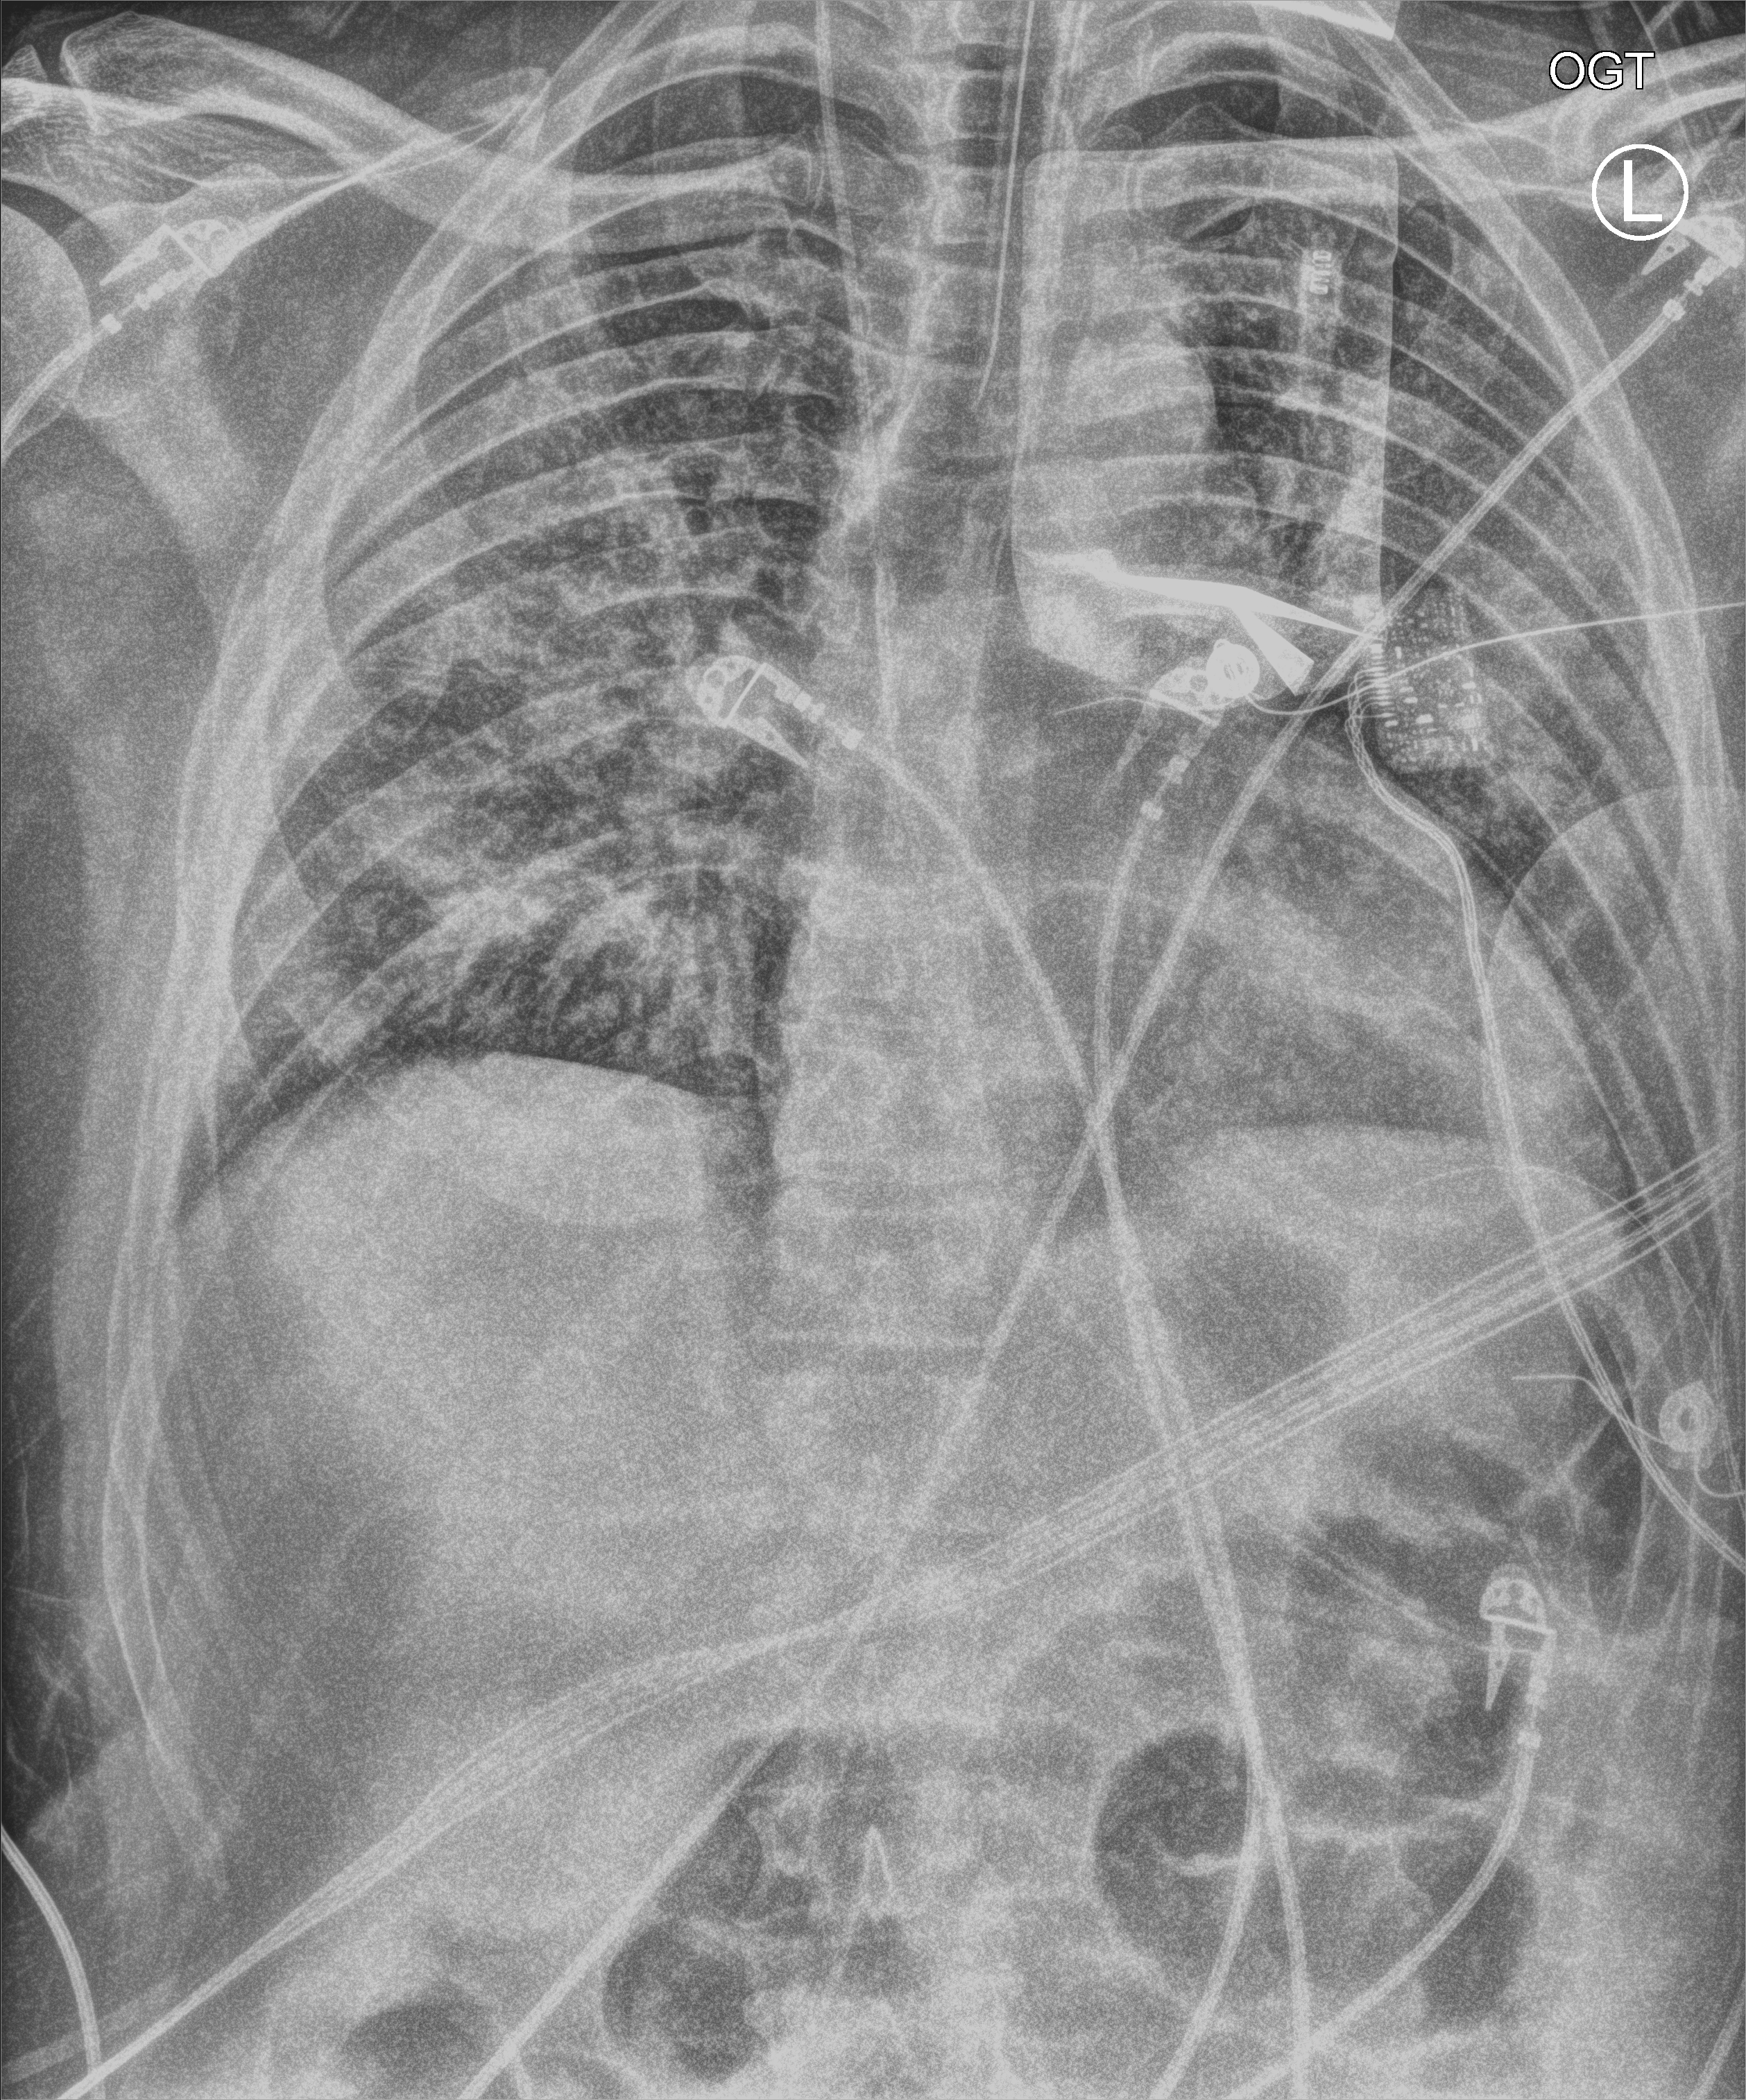
Portable chest radiograph; anteroposterior (AP) projection. Male patient hospitalised with COVID-19, age 18–59 years.
From the hospital-stay record, not from the radiograph (when in the stay this image was taken is not recorded): mechanically ventilated during this hospital stay: yes; admitted to intensive care during this hospital stay: yes.